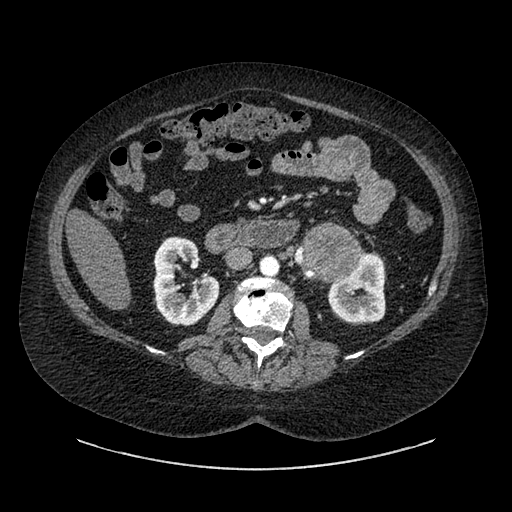
Contrast-enhanced abdominal CT, one axial slice. Slice 500 of 769 in the series (ordered by position). Intravenous contrast given. Soft-tissue window (W 400 / L 40 HU). 0.62 mm slice thickness. 512 × 512 image matrix. Patient: female, 61 years. From the clinical record (not read from this slice): diagnosis: adrenocortical carcinoma; tumour side: left adrenal; tumour size at pathology: 13 cm; Ki-67 index: 79 %; stage (as recorded): 2.
Outlined on this slice (semi-automatically segmented with operator editing):
- mass: bounding box <304,228,359,279> (left, top, right, bottom; pixels)